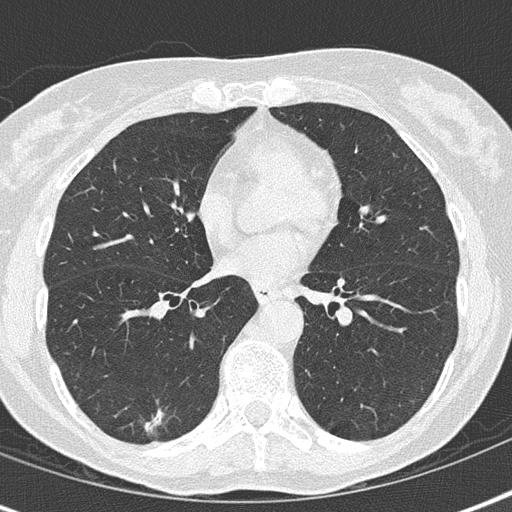
Chest CT (low-dose screening protocol), one axial image. Baseline screening round. Lung window (W 1500 / L -600 HU). 120 kVp. Slice 89 of 155 in the series. 512 × 512 image matrix. Female participant, aged 69 years at enrolment.
Expert reader's lesion annotation, bounding box (x1, y1, x2, y2) in pixels: (118, 392, 181, 451). The screening reader recorded 2 non-calcified nodules or masses ≥4 mm on this exam (right lower lobe, left lower lobe); which of them this box marks is not recorded. Lung cancer was diagnosed 476 days after this screen: adenocarcinoma, NOS, right lower lobe, moderately differentiated (G2), stage IA (AJCC 6th edition), 16 mm at pathology.